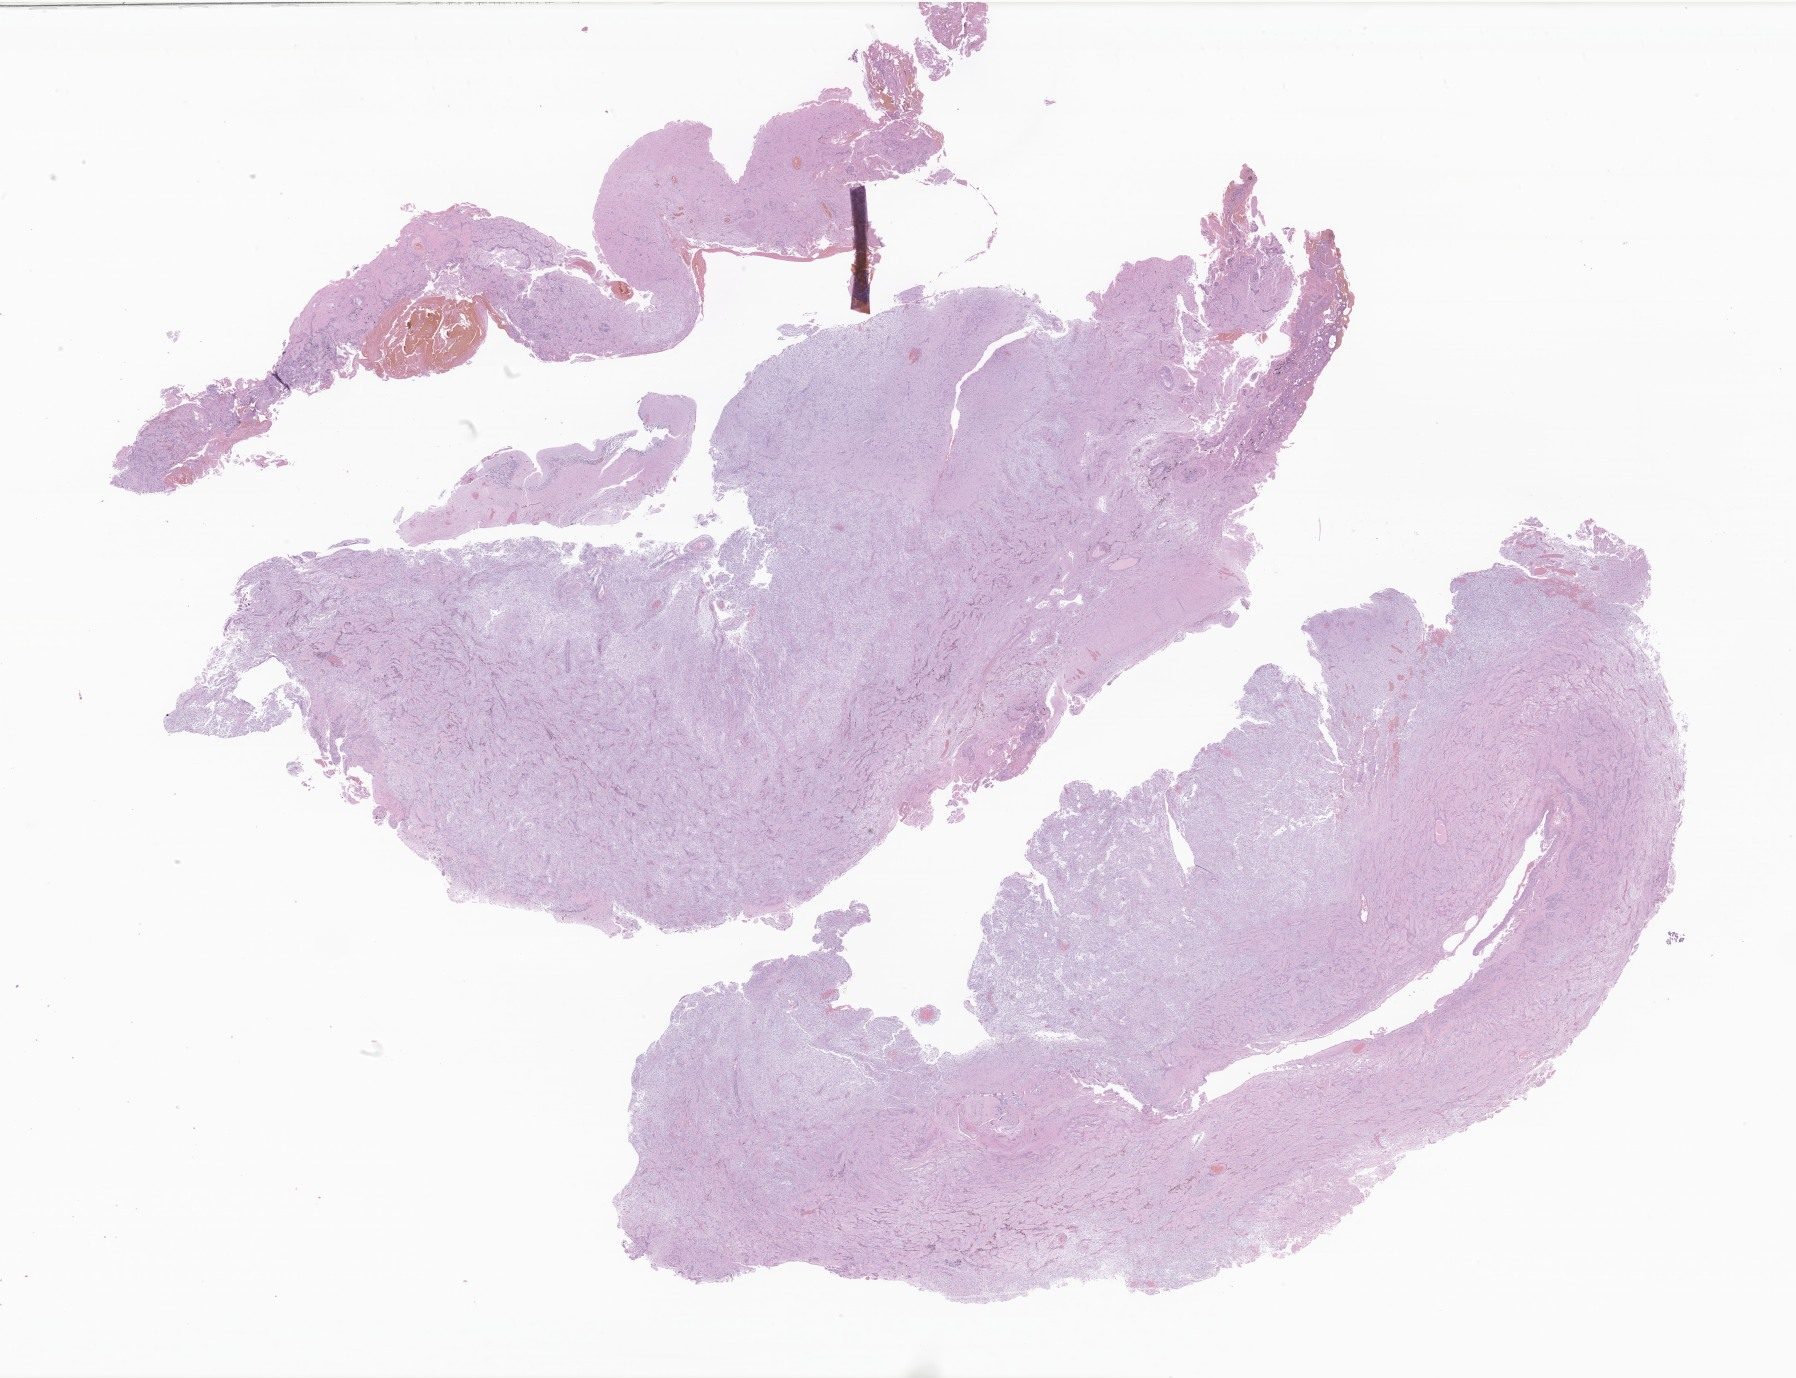
H&E whole-slide image of tumor tissue from the cerebellum — whole scanned area (about 30.3 x 23.2 mm) shown as a low-resolution overview, formalin-fixed, paraffin-embedded (FFPE) tissue. Male patient, age 61 months (5 years 1 month).
Diagnosis: Pilocytic astrocytoma.